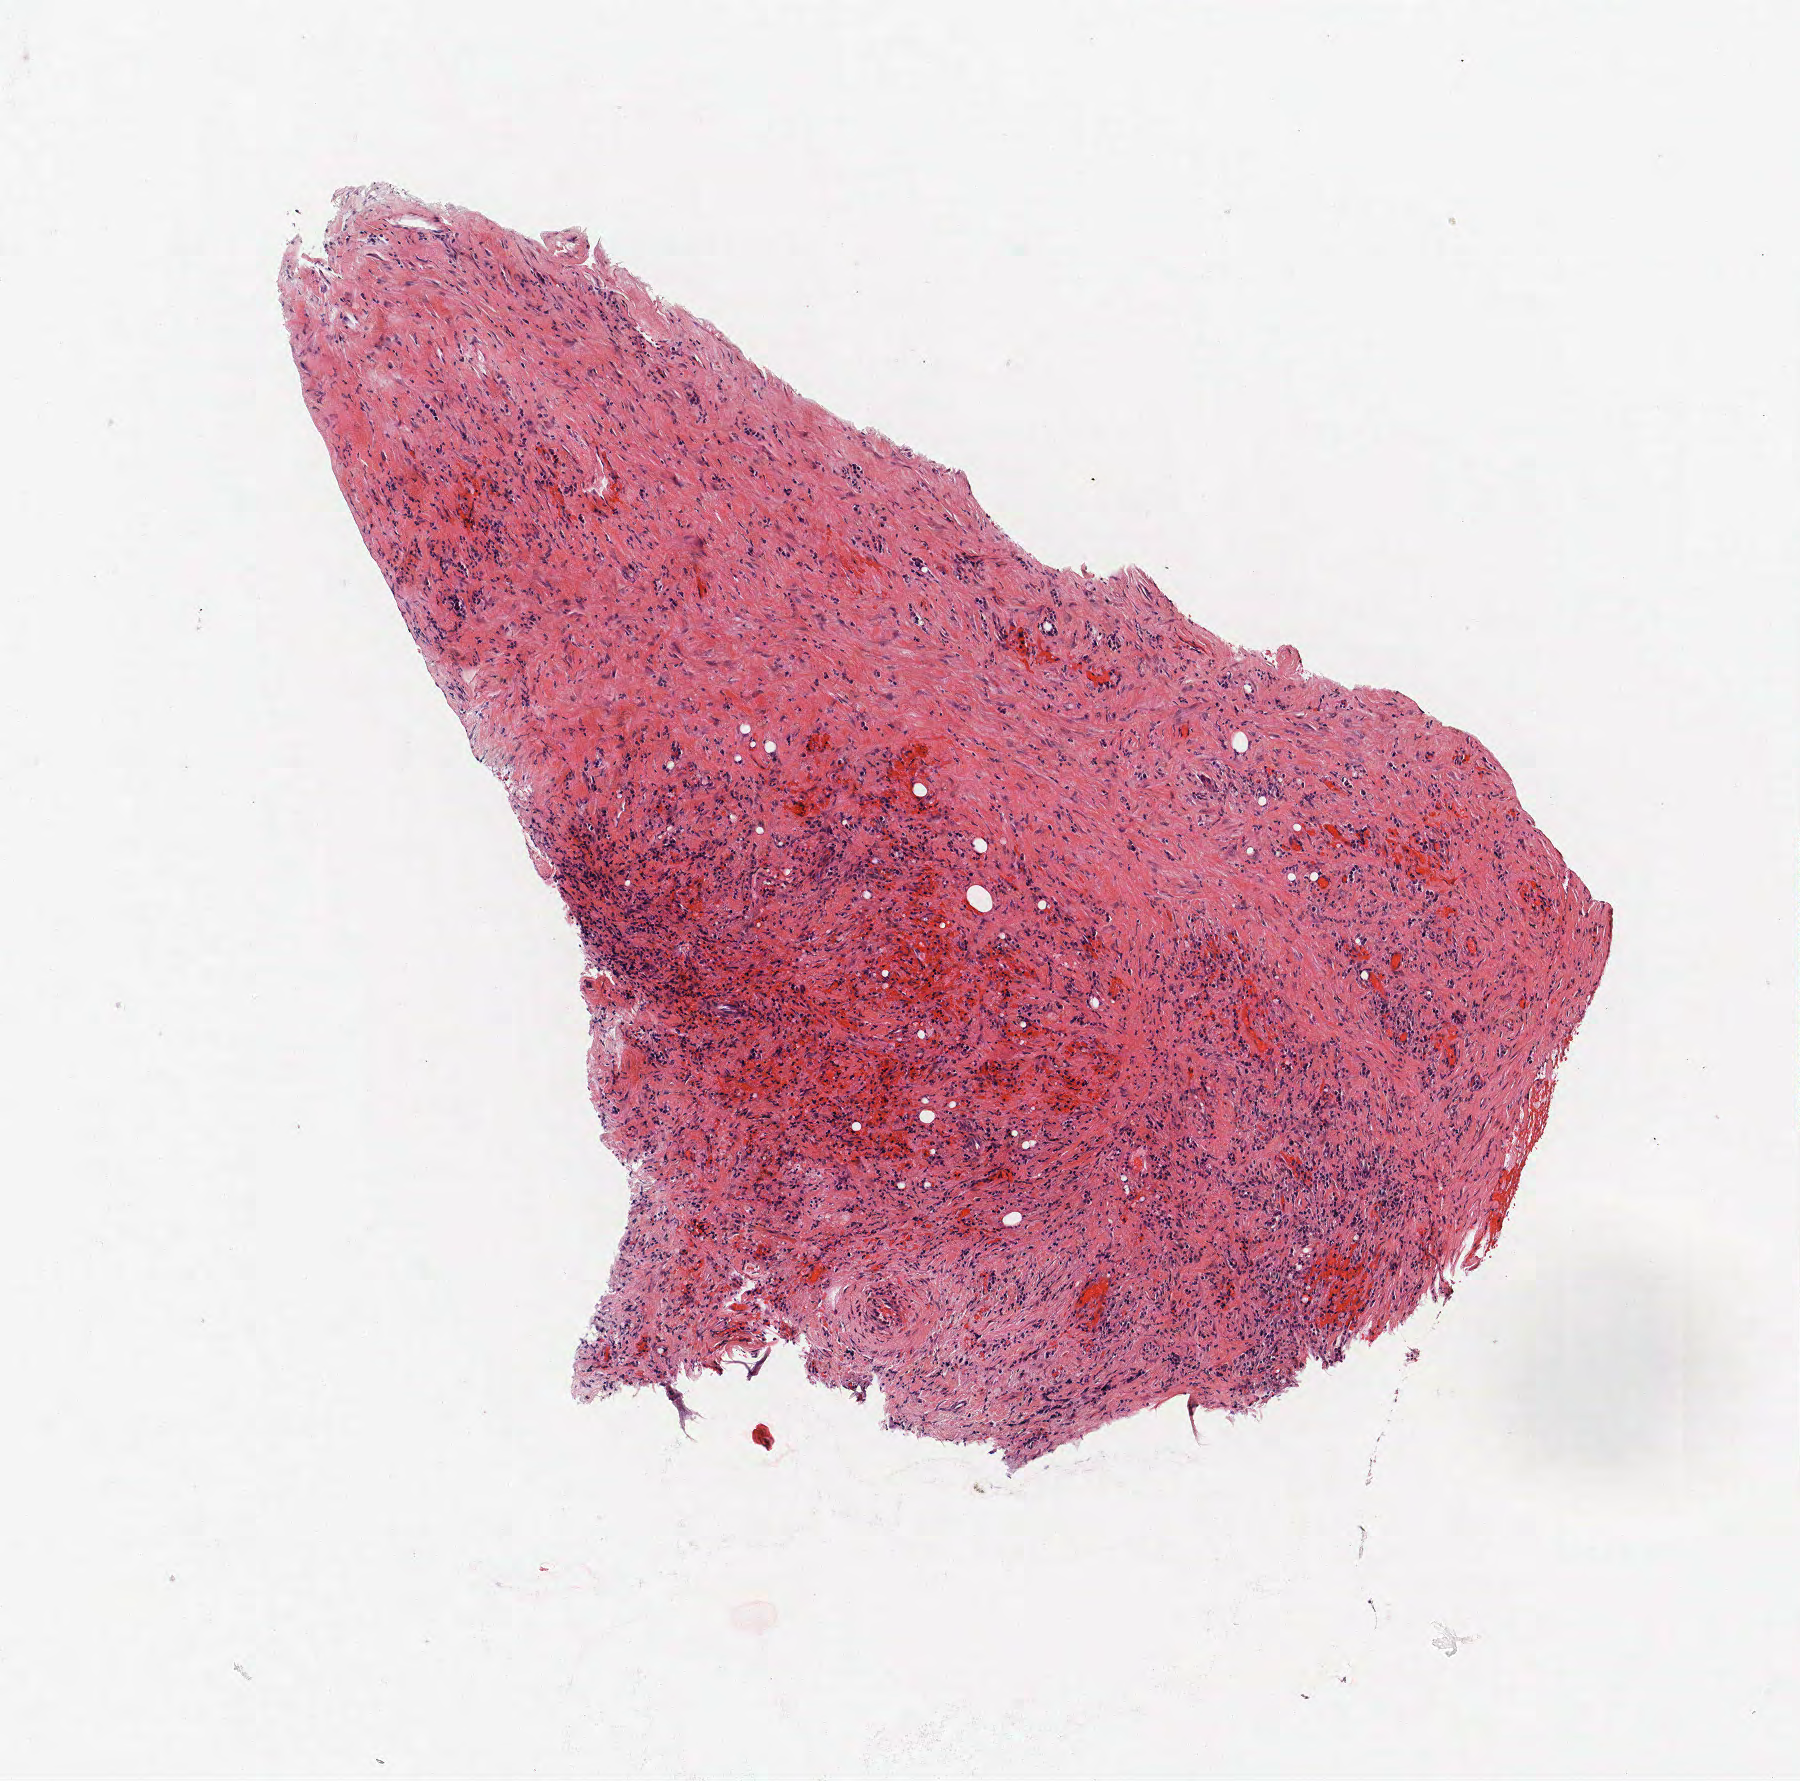
H&E-stained whole-slide image, a low-resolution overview of the entire scanned area, about 3.6 x 3.6 mm, FFPE section, lung tissue. Male, age 56 at enrolment. Current smoker at enrolment. Grade: cannot be assessed (GX).
• tumour size (pathology): 20 mm
• participant's lung-cancer diagnosis: Squamous cell carcinoma, NOS
• stage (AJCC 6th edition): IIIA
• primary tumour location (clinical record): right upper lobe